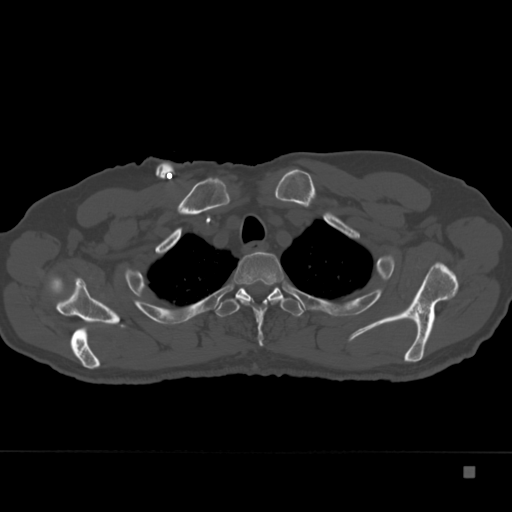
CT including the spine, one axial slice. Slice 294 of 332 in the series (ordered by position). Bone window (W 1800 / L 400 HU). 512 × 512 image matrix, field of view 389 × 389 mm. Patient: male, 72 years. From the clinical record (not read from this slice): primary cancer: skeletal.
Annotated regions visible in this slice (semi-automatic segmentation, software-assisted and operator-edited):
- T2 vertebra: bounding box <234,251,284,346> (left, top, right, bottom; pixels)
- T3 vertebra: <215,287,304,317>